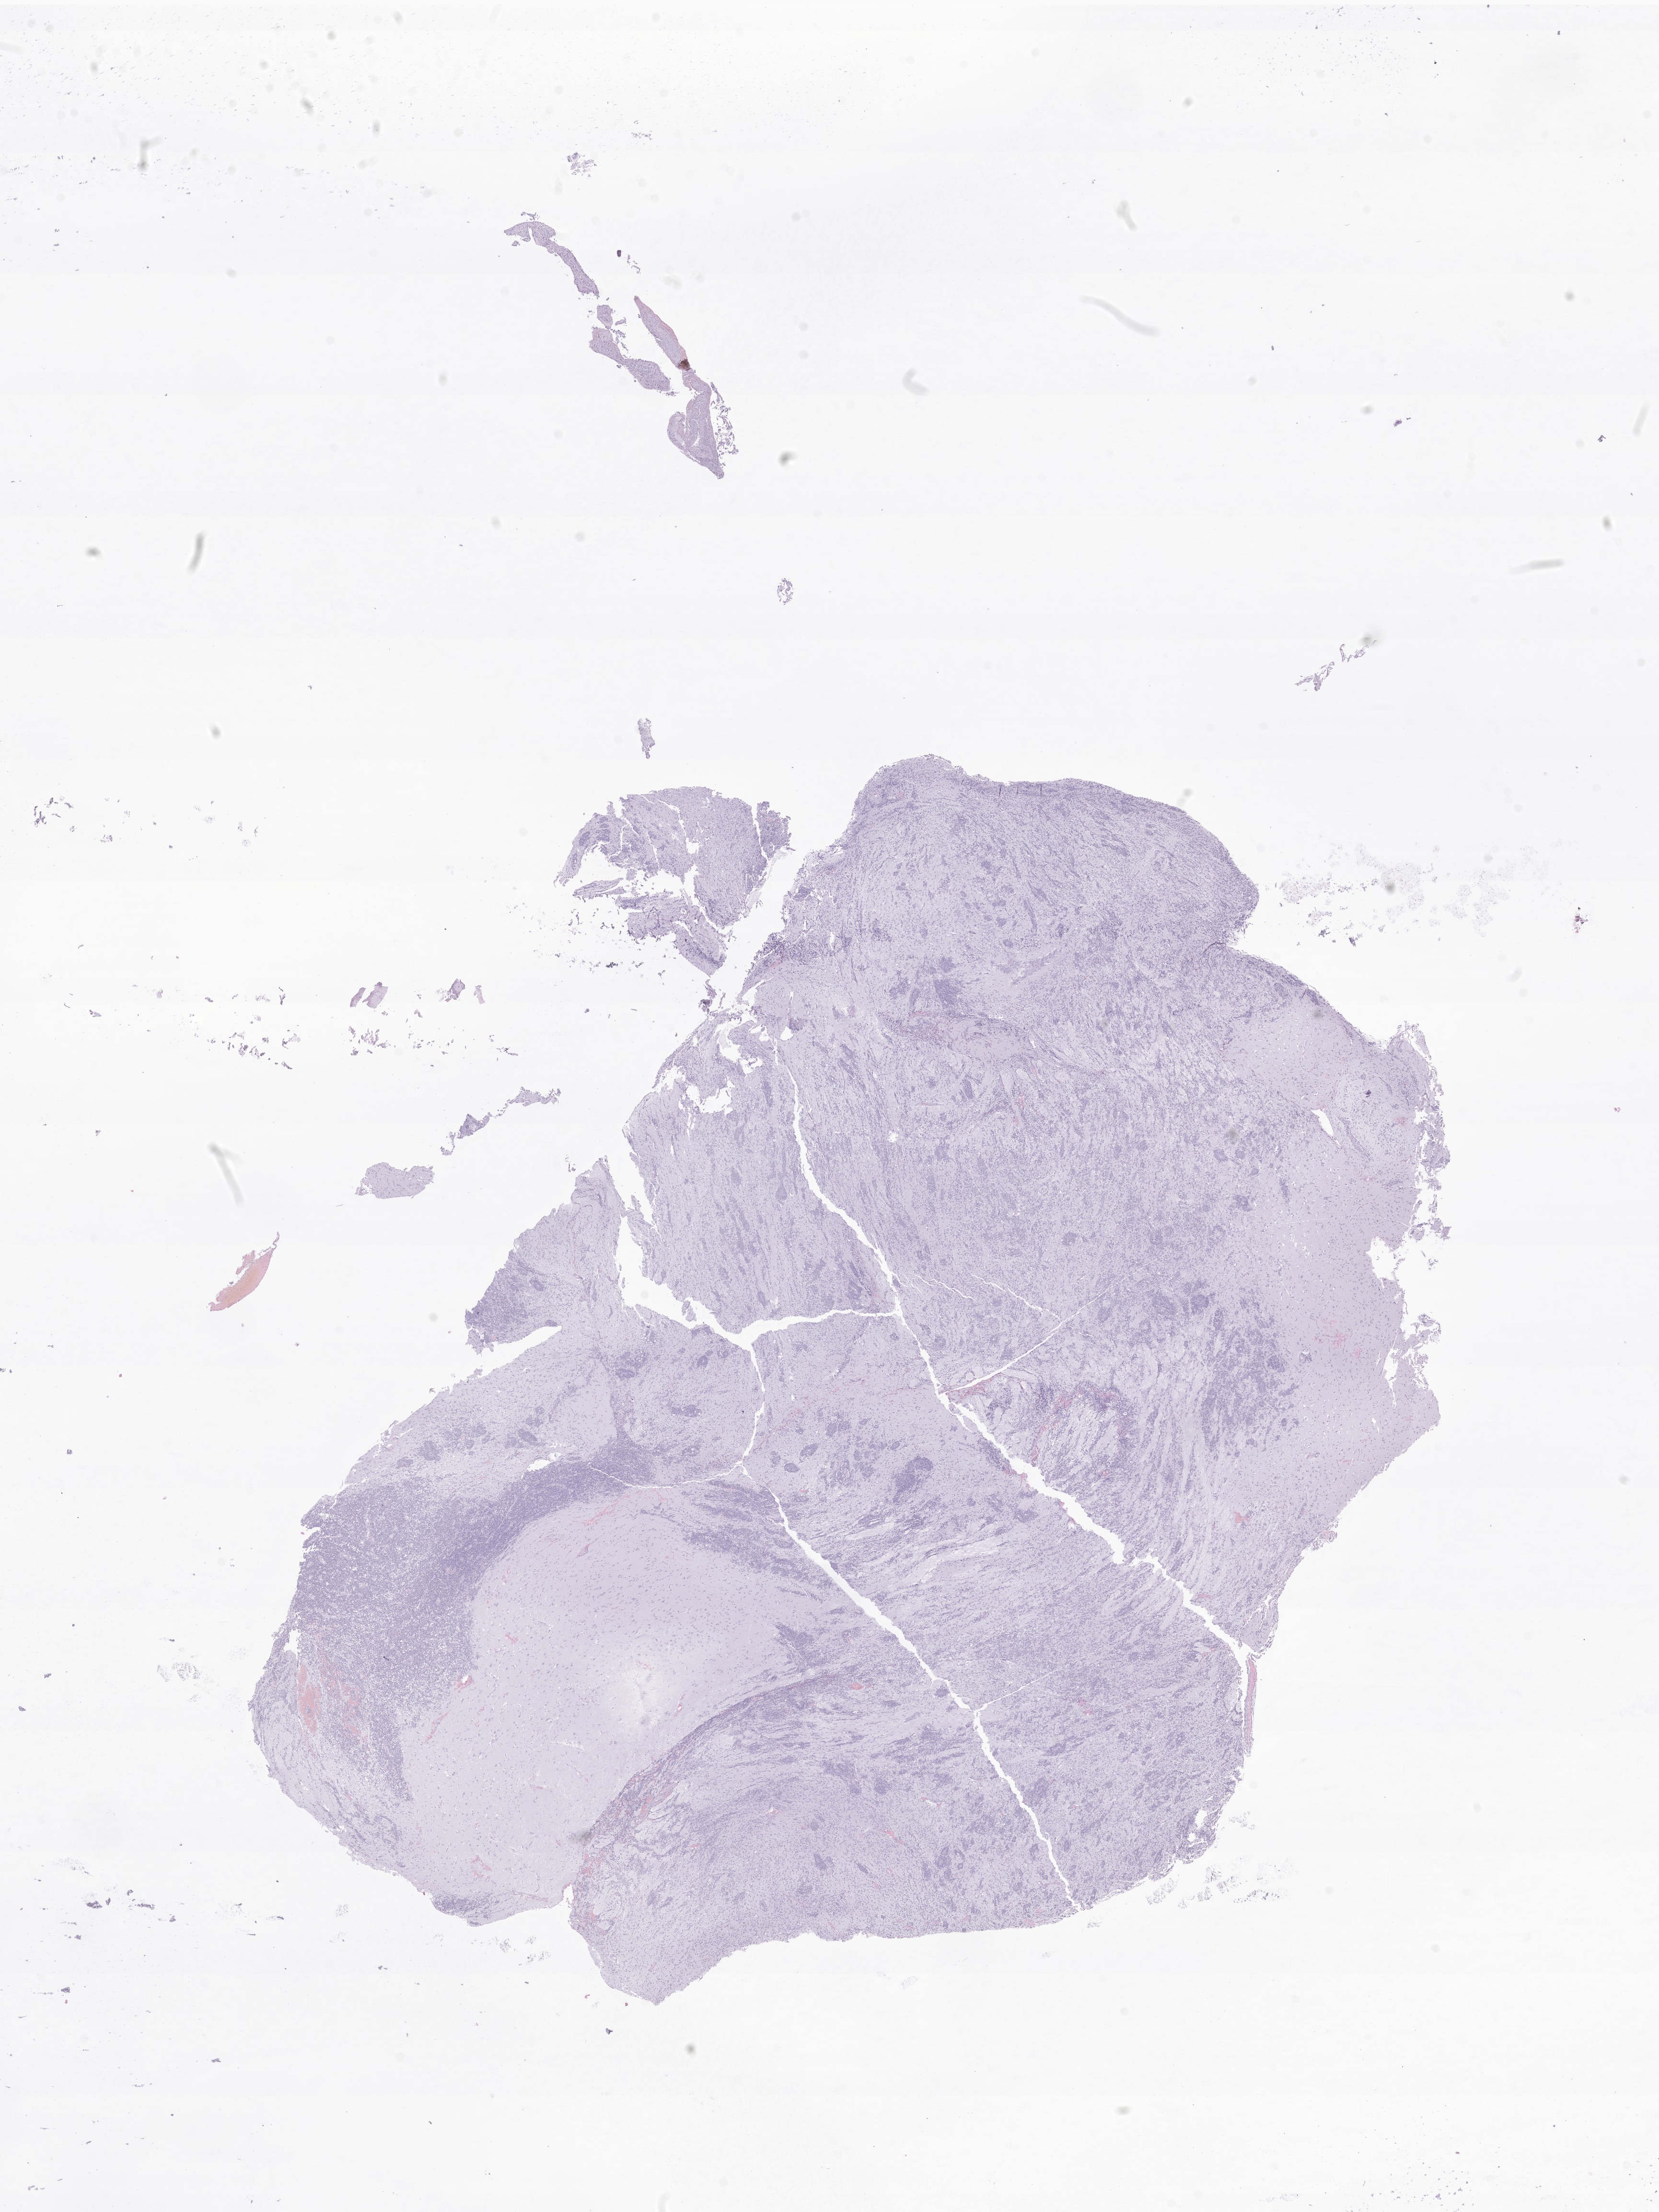
Haematoxylin and eosin whole-slide image of tumor tissue from the frontal lobe, low-resolution overview of the scanned area, about 14.6 x 19.5 mm, formalin-fixed, paraffin-embedded (FFPE) tissue. Patient: female, age 38 months (3 years 2 months).
Recorded diagnosis: CNS embryonal tumor, NOS.